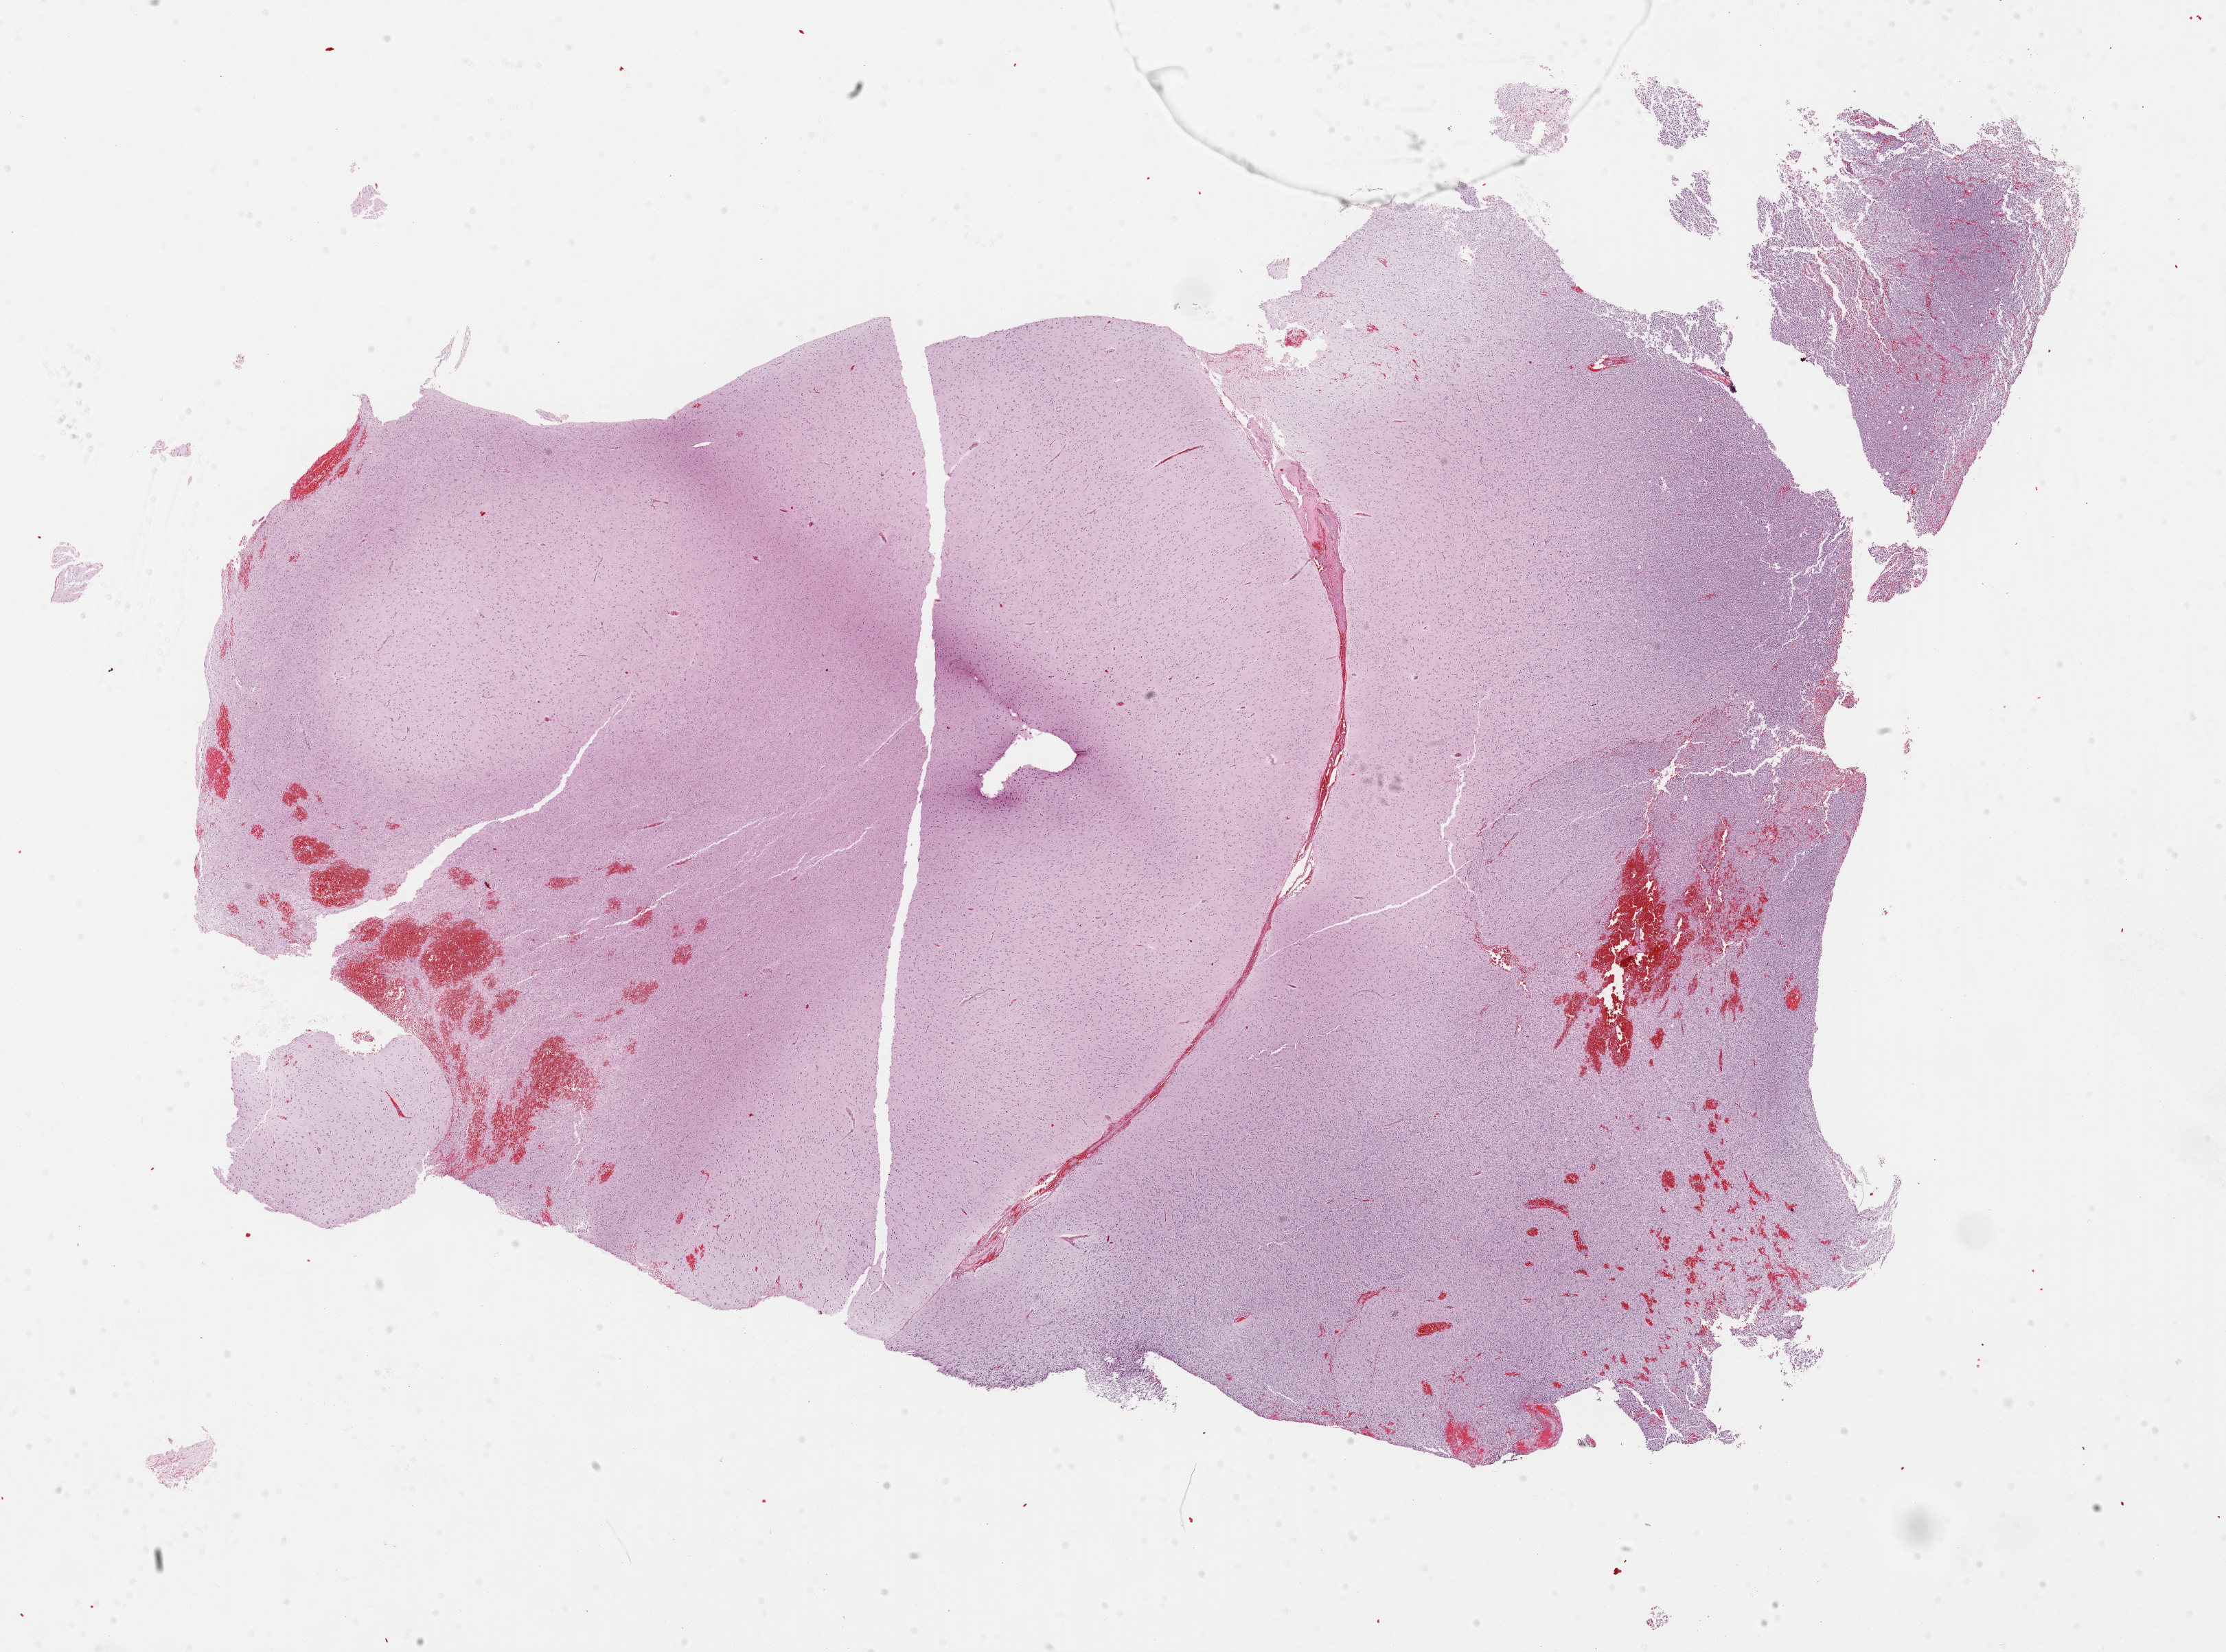
Digitized H&E tissue section (whole slide), a low-resolution overview of the entire scanned area, about 25.6 x 19.0 mm (slide scanned at 40x). Formalin-fixed paraffin-embedded (FFPE) diagnostic section. Brain, primary tumour sample. Male patient; age at initial diagnosis 68 years.
Pathologic diagnosis: Oligodendroglioma, anaplastic (cerebrum).